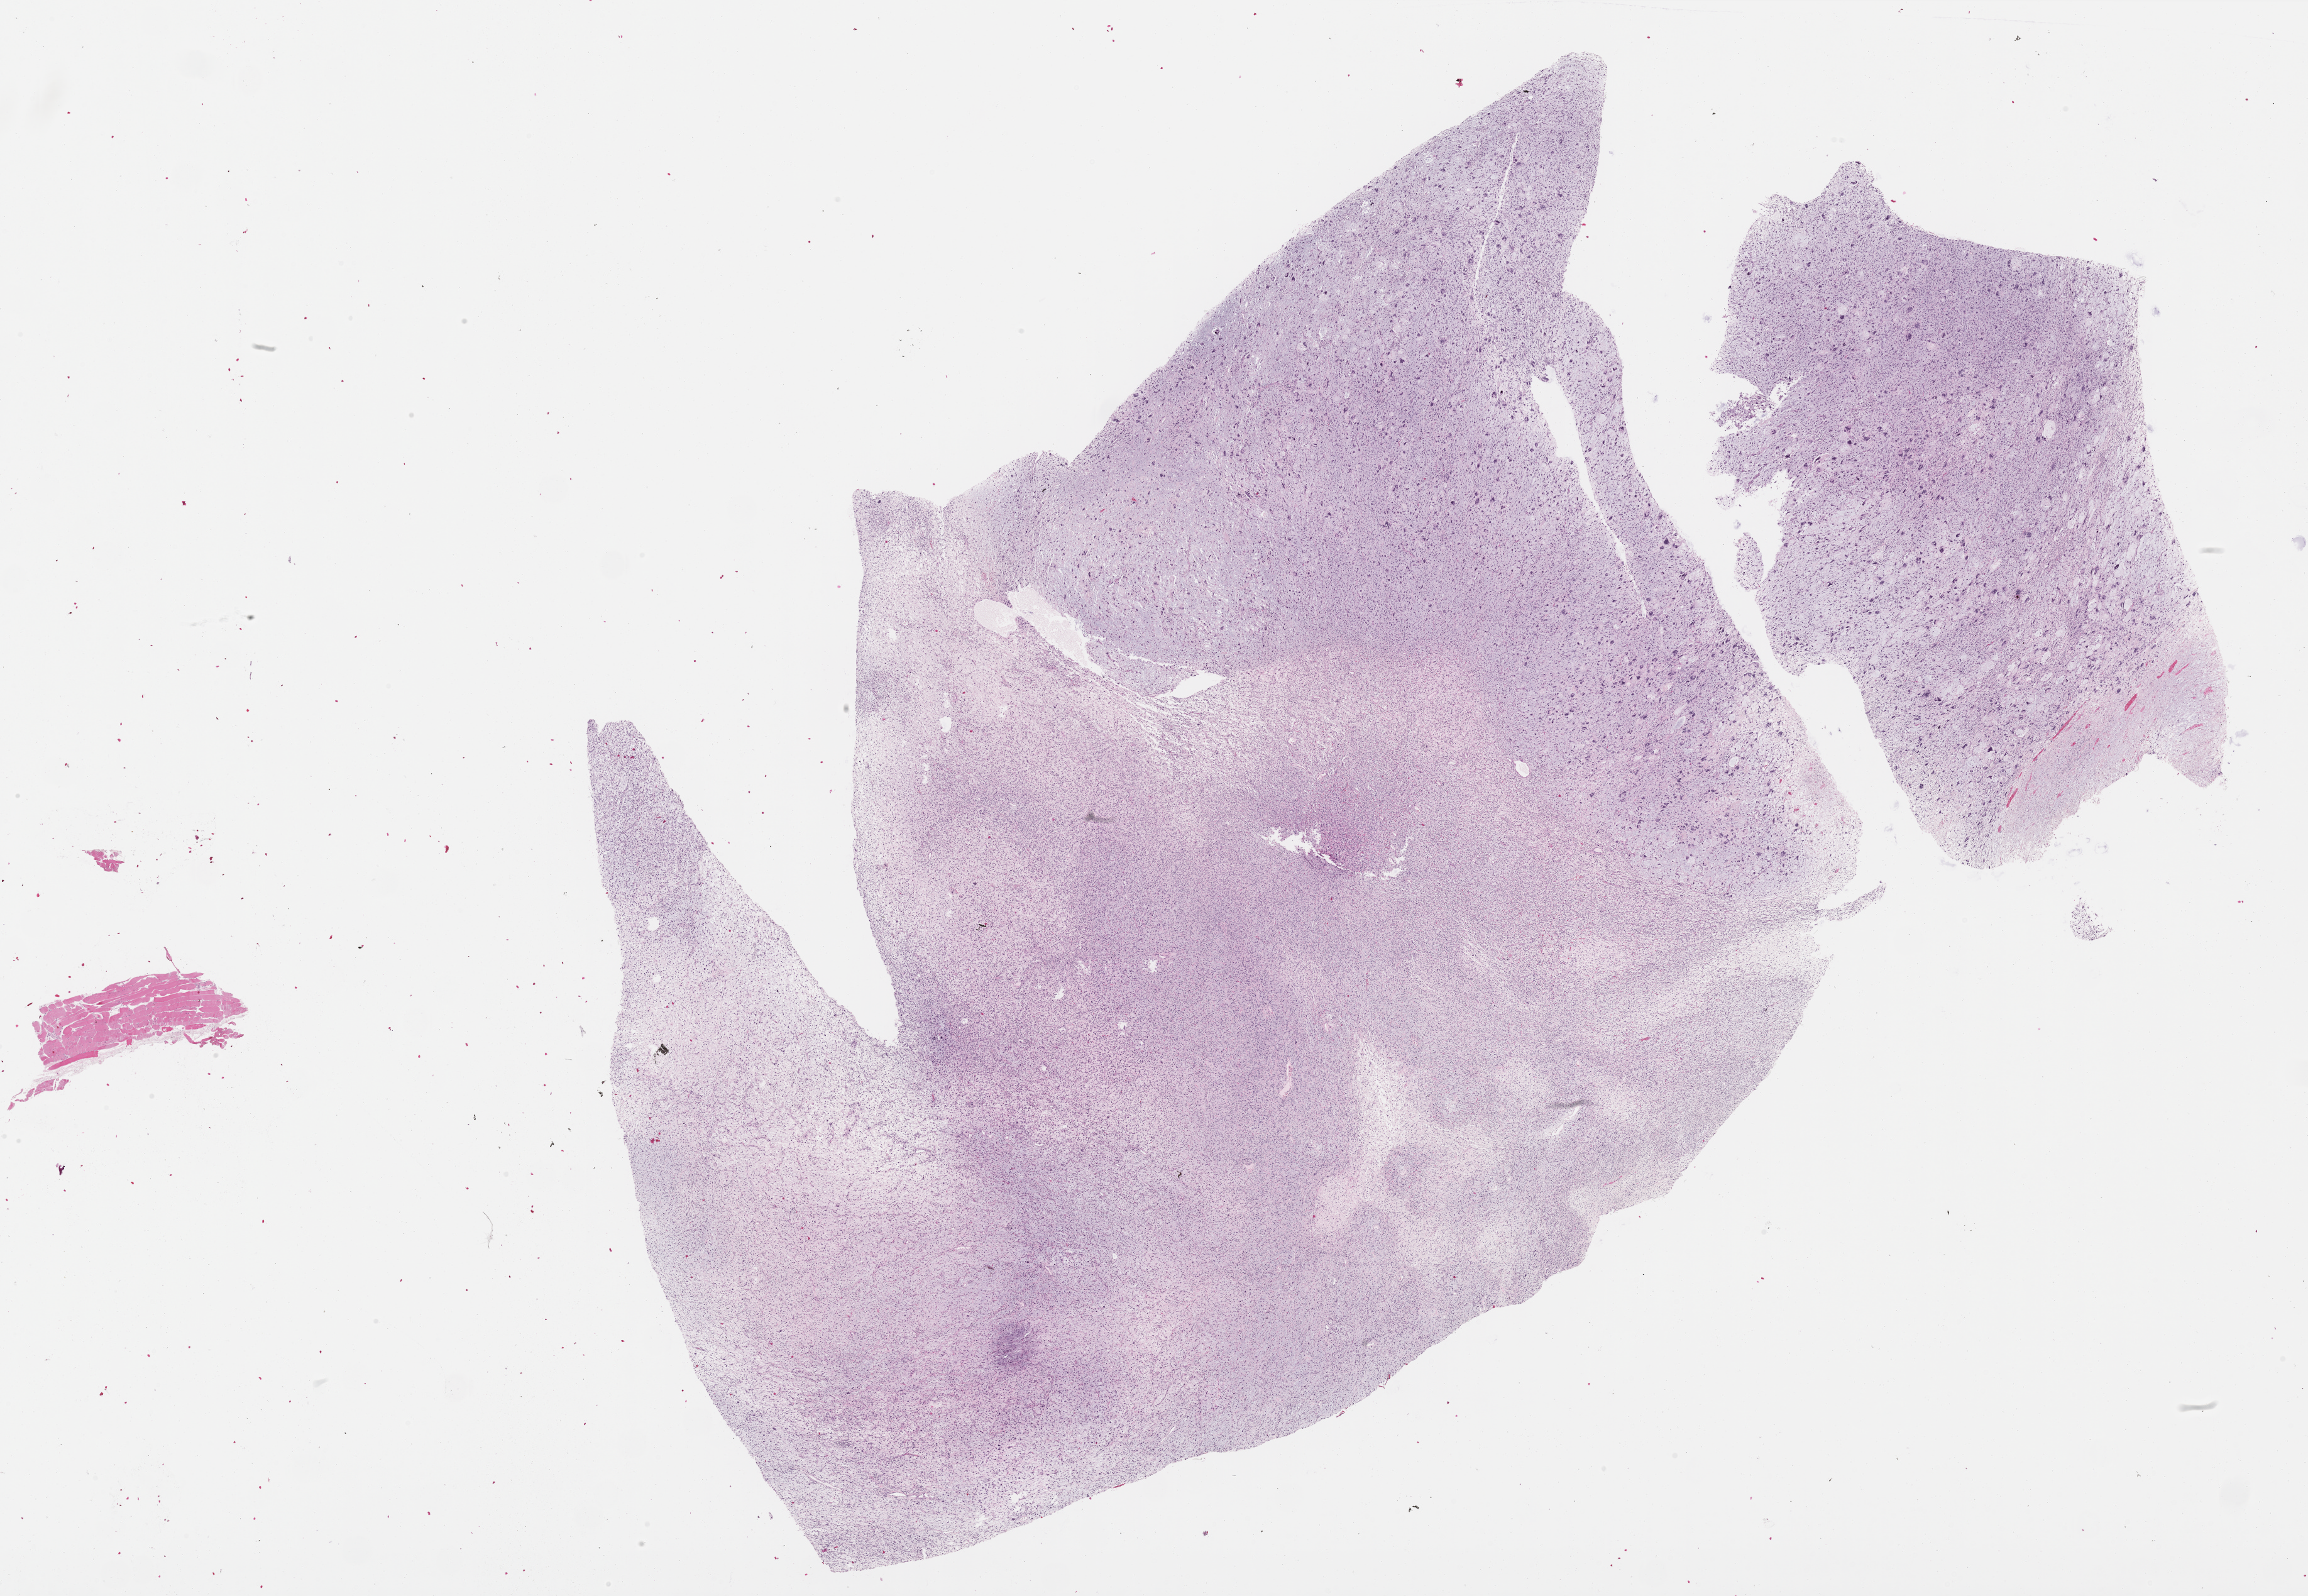
Hematoxylin and eosin (H&E) stained whole-slide image — shown as a low-resolution overview of the whole scanned area (about 29.7 x 20.5 mm, acquisition: 40x scan), formalin-fixed paraffin-embedded (FFPE) diagnostic section, primary tumour sample from the connective, subcutaneous and other soft tissues. Female patient; age at initial diagnosis 50 years.
- pathologic diagnosis: Fibromyxosarcoma (connective, subcutaneous and other soft tissues of thorax)